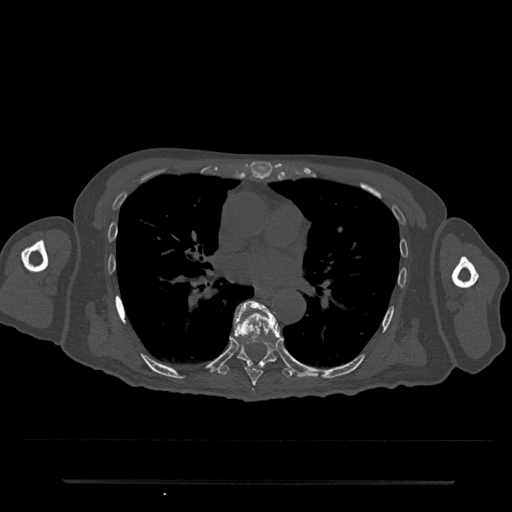
CT including the spine, one axial slice; slice 453 of 797 in the series (ordered by position); 120 kVp; bone window (W 1800 / L 400 HU); 0.5 mm slice thickness; 512 × 512 image matrix, field of view 427 × 427 mm. Patient: male, 74 years. From the clinical record (not read from this slice): primary cancer: prostate.
Outlined on this slice (semi-automatic segmentation, software-assisted and operator-edited):
- T7 vertebra: bounding box (x1, y1, x2, y2) in pixels: (234, 301, 283, 386)
- T8 vertebra: (217, 328, 294, 378)